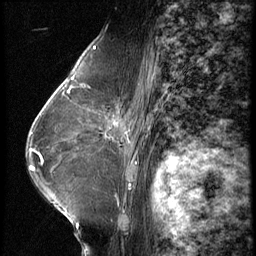
Breast MRI (dynamic contrast-enhanced), one sagittal slice. Position 39 of 62 along the scan axis. 3 images stored at this slice position (order not interpretable as contrast timing). 1.5 T. TE 4.2 ms, TR 9 ms. 256 × 256 image matrix, field of view 180 × 180 mm. Patient: female, 65 years. From the clinical record (not read from this slice): setting: breast cancer imaged before/during neoadjuvant chemotherapy; receptor status: HR-positive, HER2-negative.
Structures marked on this image (semi-automatically segmented with operator editing):
- analysis volume of interest (the breast-tissue region the enhancement analysis was run in; not a lesion): bounding box <104,104,154,161> (left, top, right, bottom; pixels)
- tumour enhancement mask (voxels above the 140 % enhancement threshold inside the analysis volume of interest): <105,123,116,138>